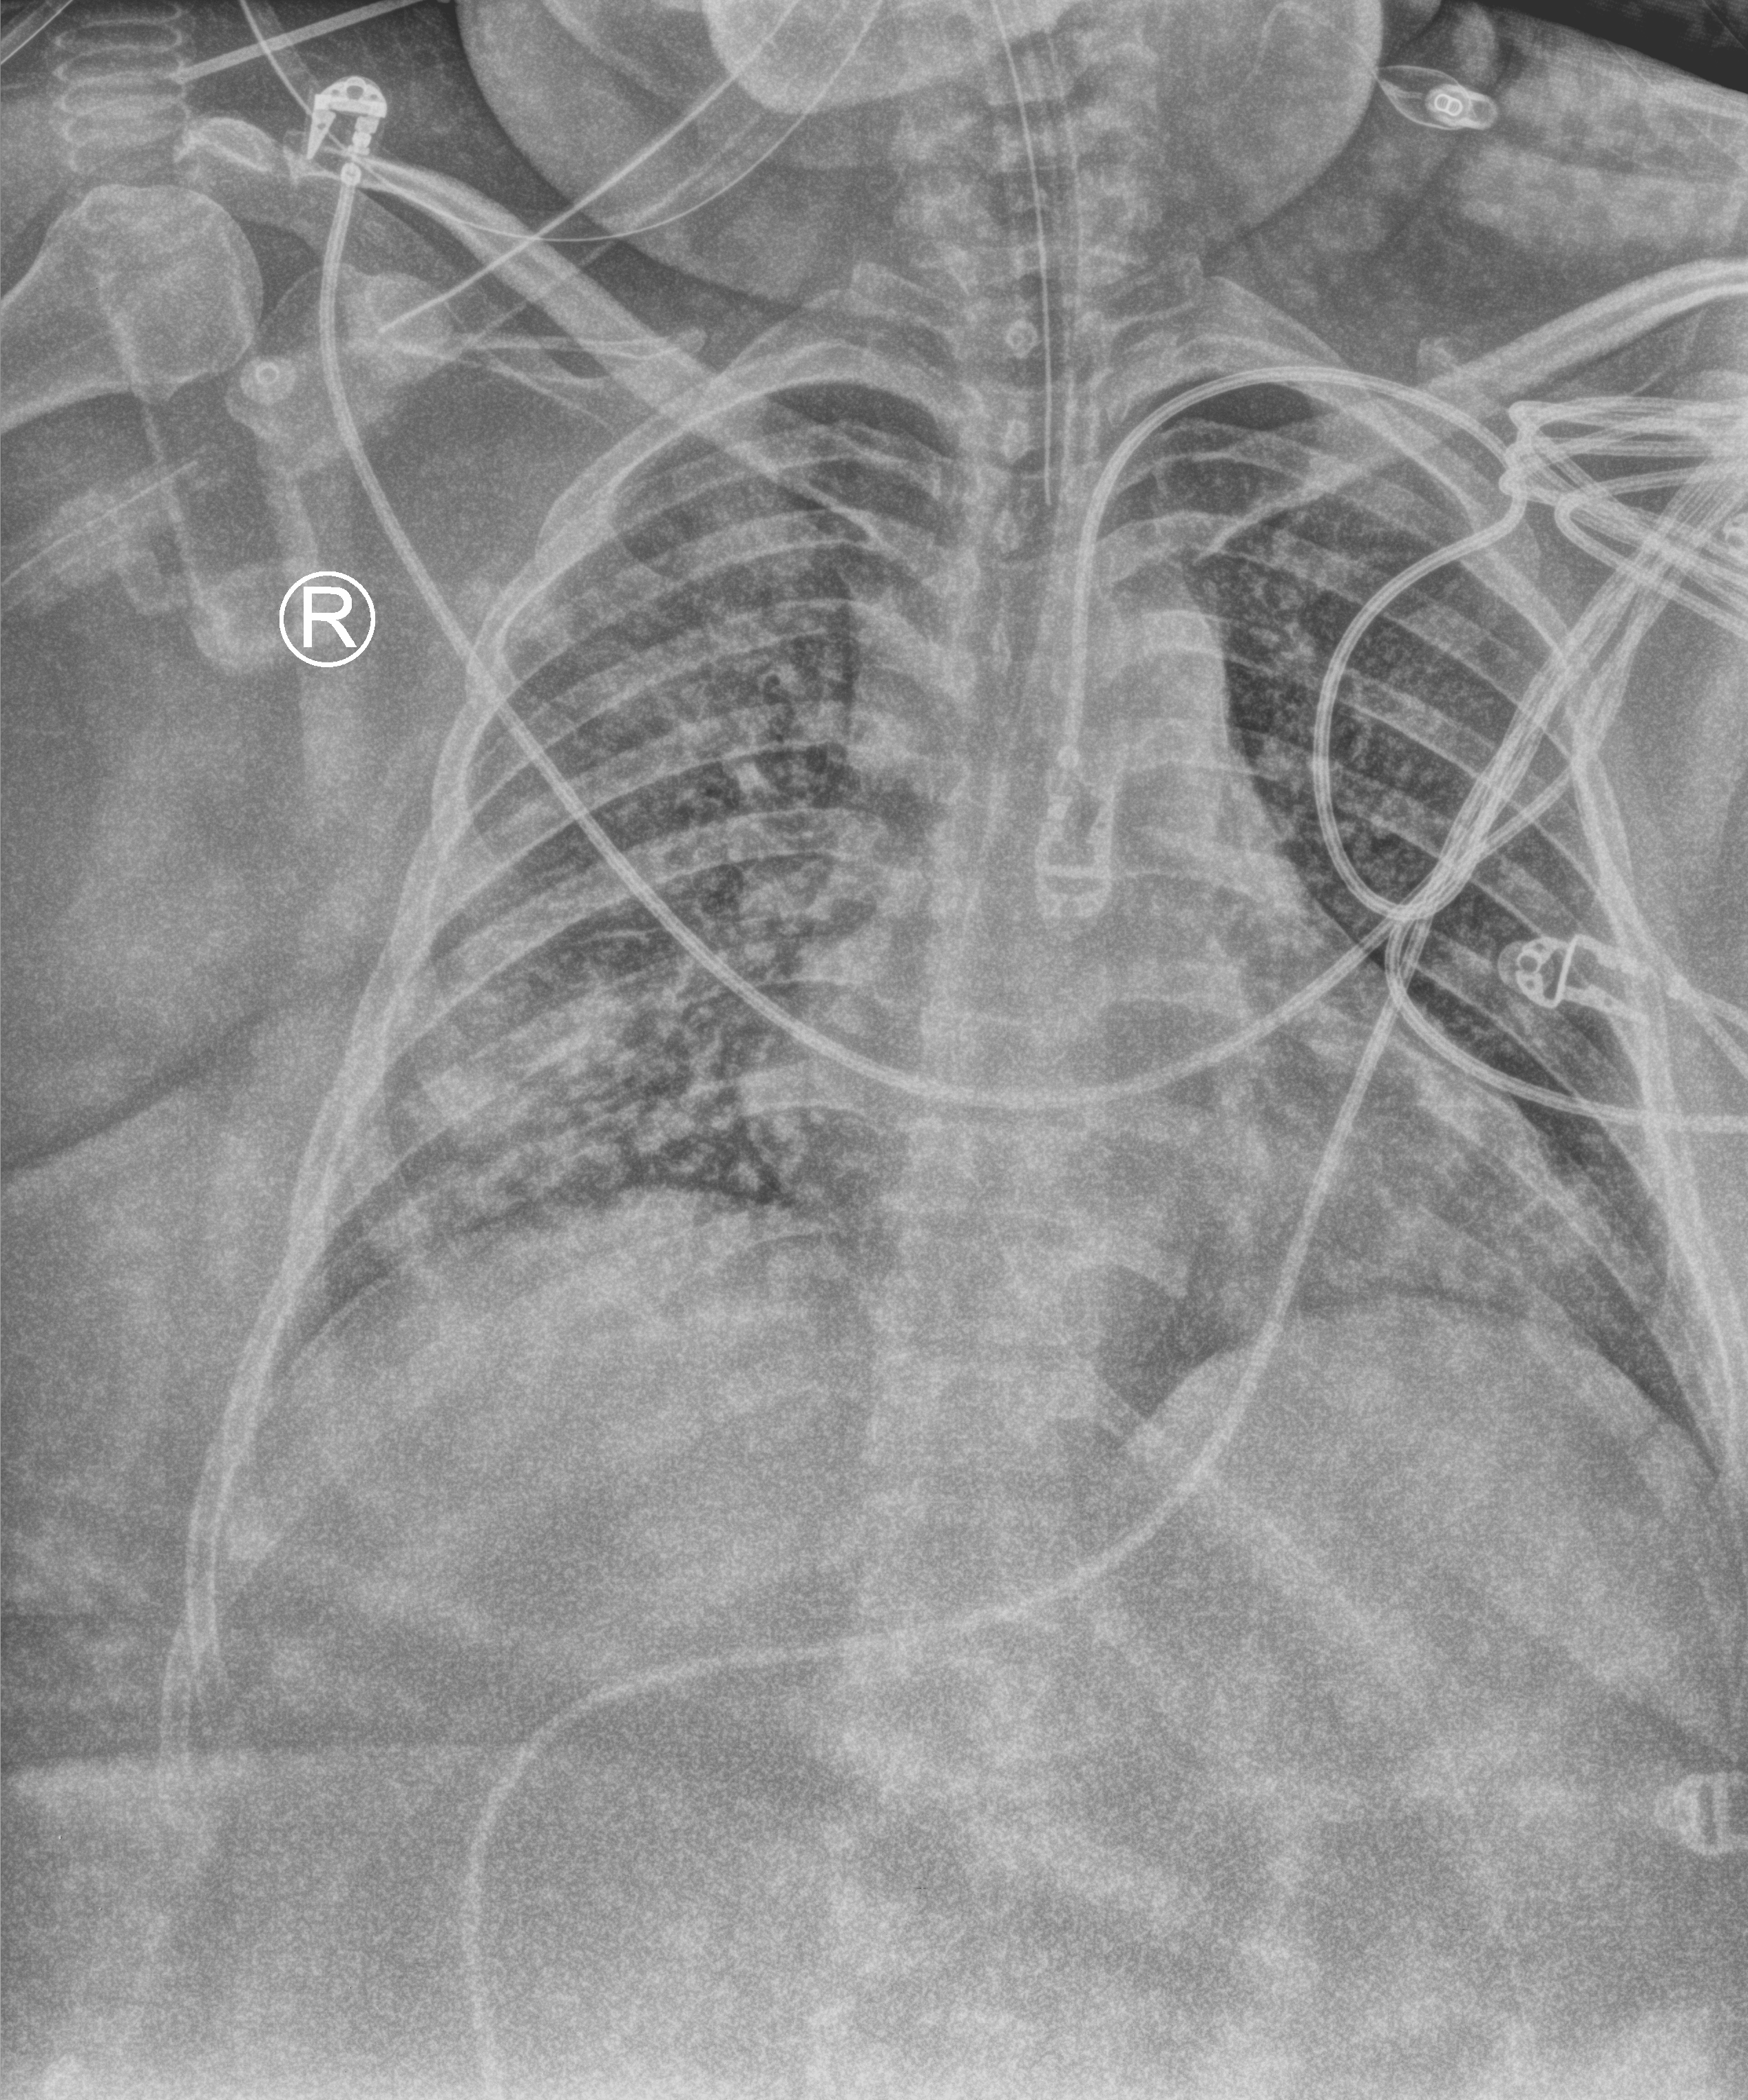
Chest X-ray (portable), anteroposterior (AP) projection. Patient hospitalised with COVID-19; female, aged 18–59 years.
Admission-level facts for this patient (not findings on this image; timing relative to this image not recorded): smoking status (admission record): former.